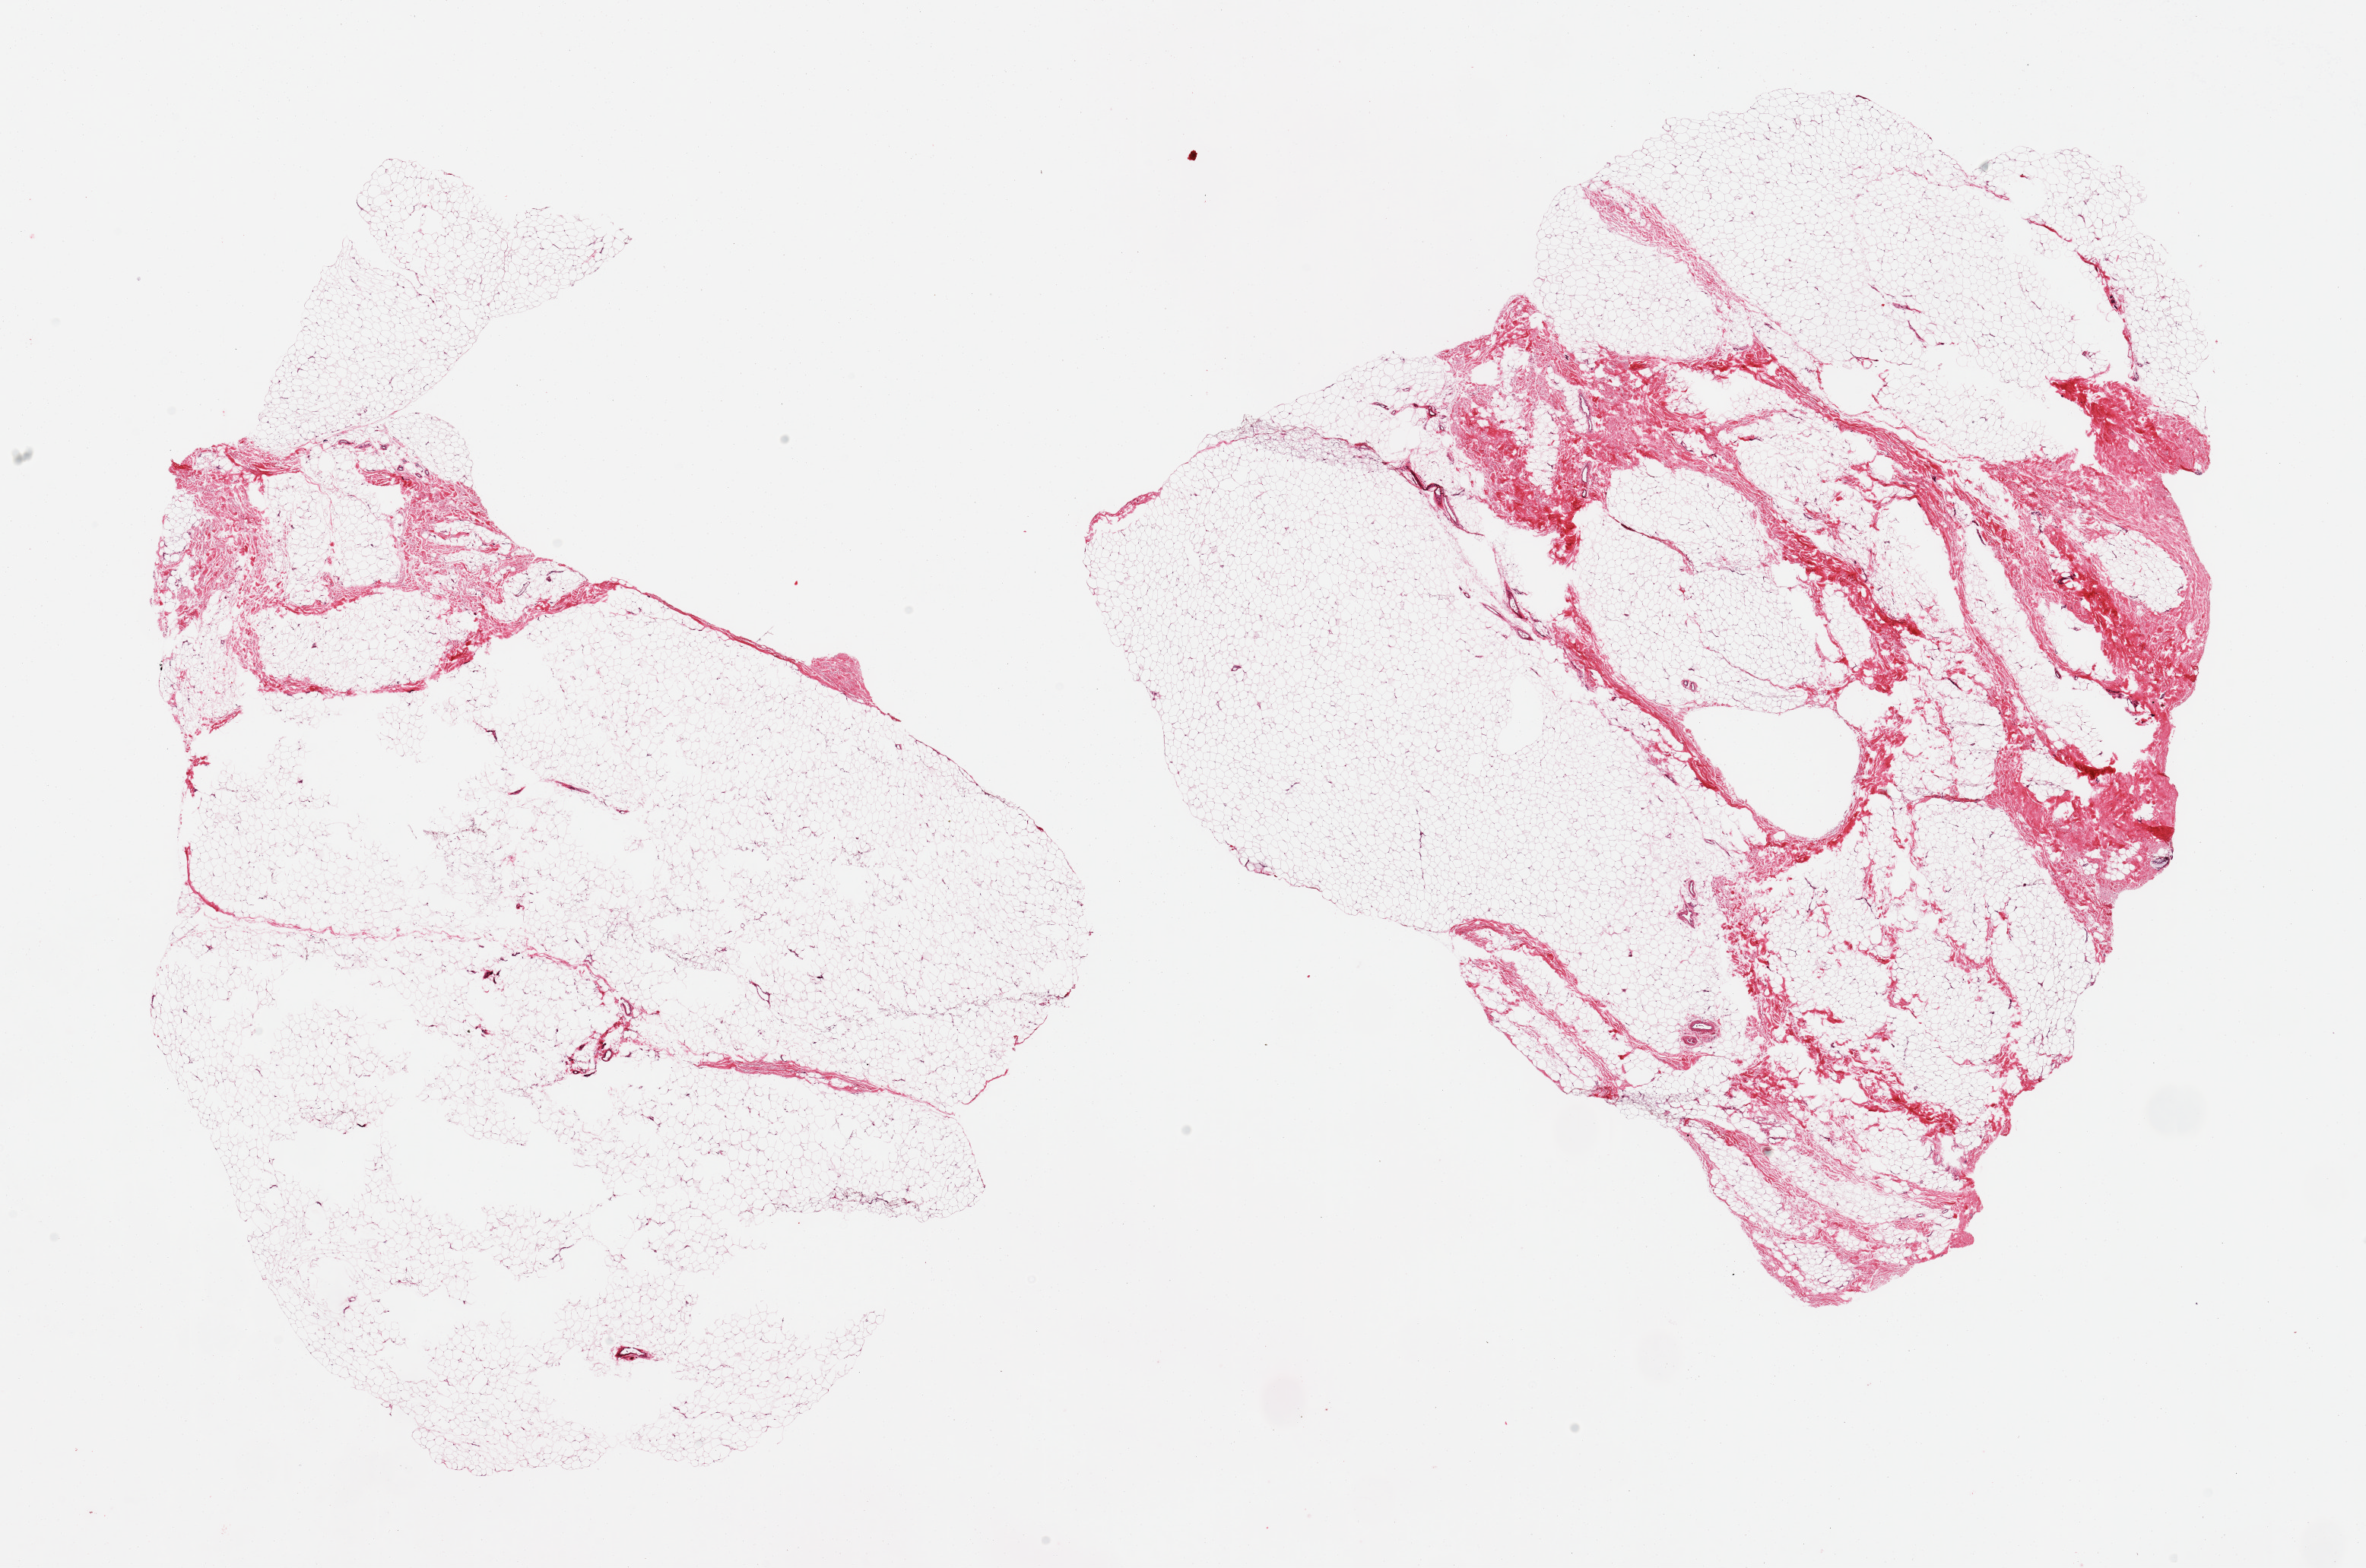
Whole-slide image, haematoxylin and eosin stain, brightfield, shown as a low-resolution overview of the whole scanned area (about 24.6 x 16.3 mm, slide scanned at 20x), PAXgene-fixed, paraffin-embedded tissue, section of breast (target tissue), donor tissue sample.
Review note (as recorded): 2 pieces; fibrofatty tissue without mammary ducts.